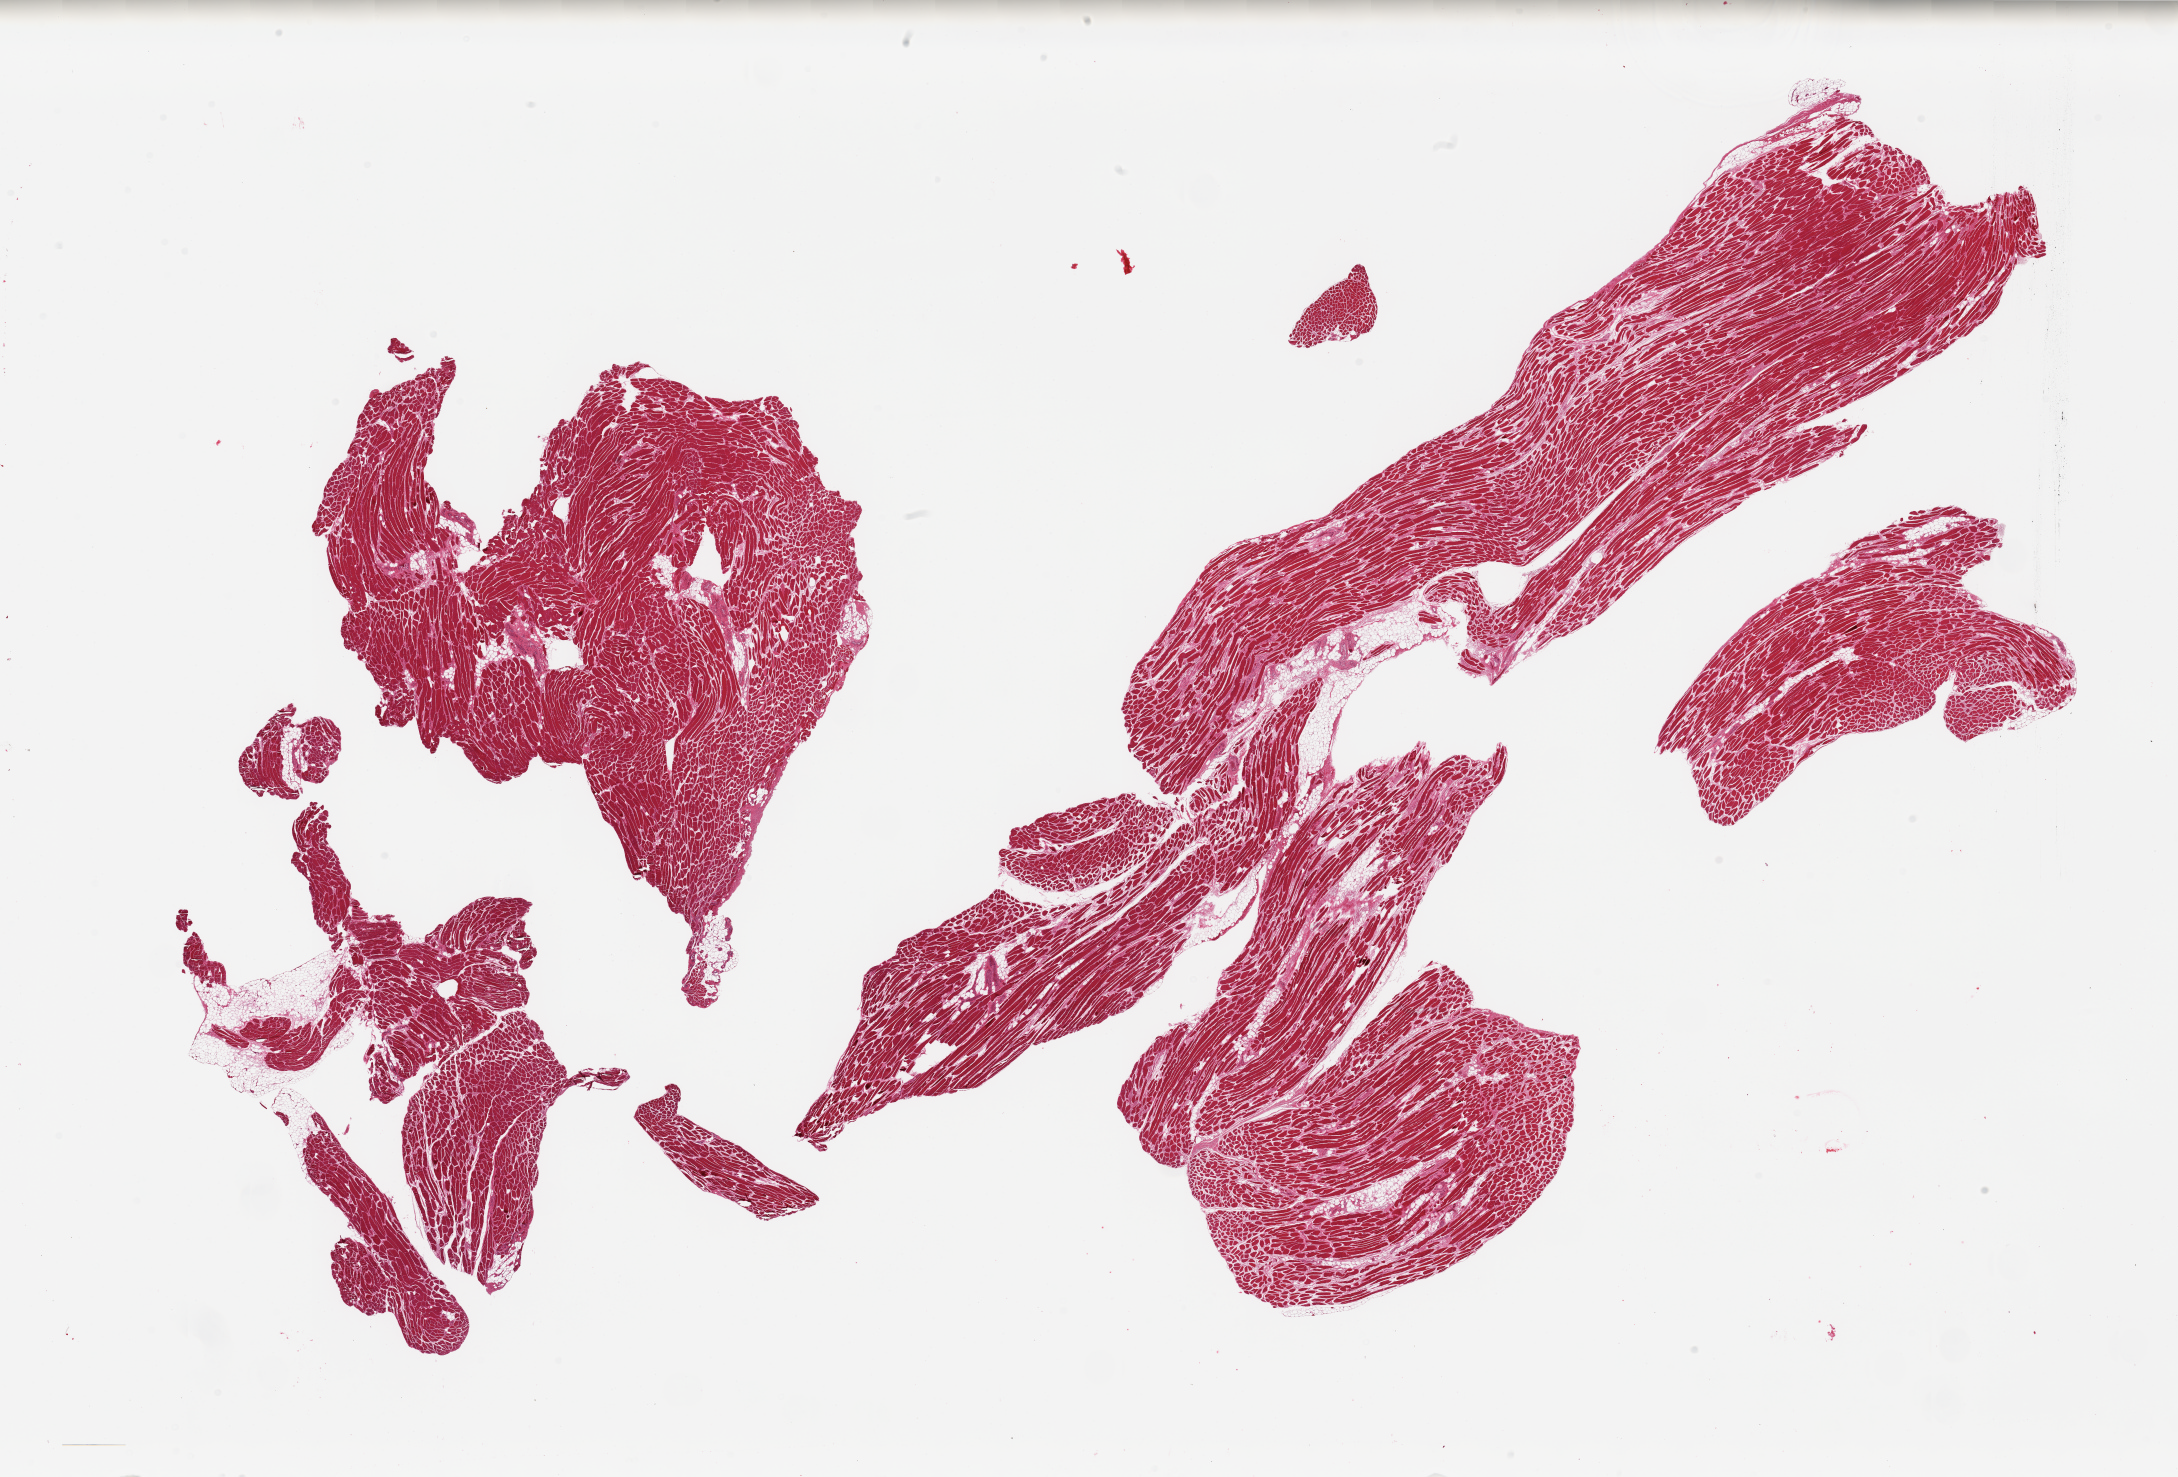
Haematoxylin and eosin whole-slide image — shown as a low-resolution overview of the whole scanned area (about 34.5 x 23.4 mm, slide scanned at 20x); PAXgene-fixed, paraffin-embedded tissue; section of skeletal muscle (target tissue); donor tissue sample.
* review note (as recorded): 2 fragmented pieces